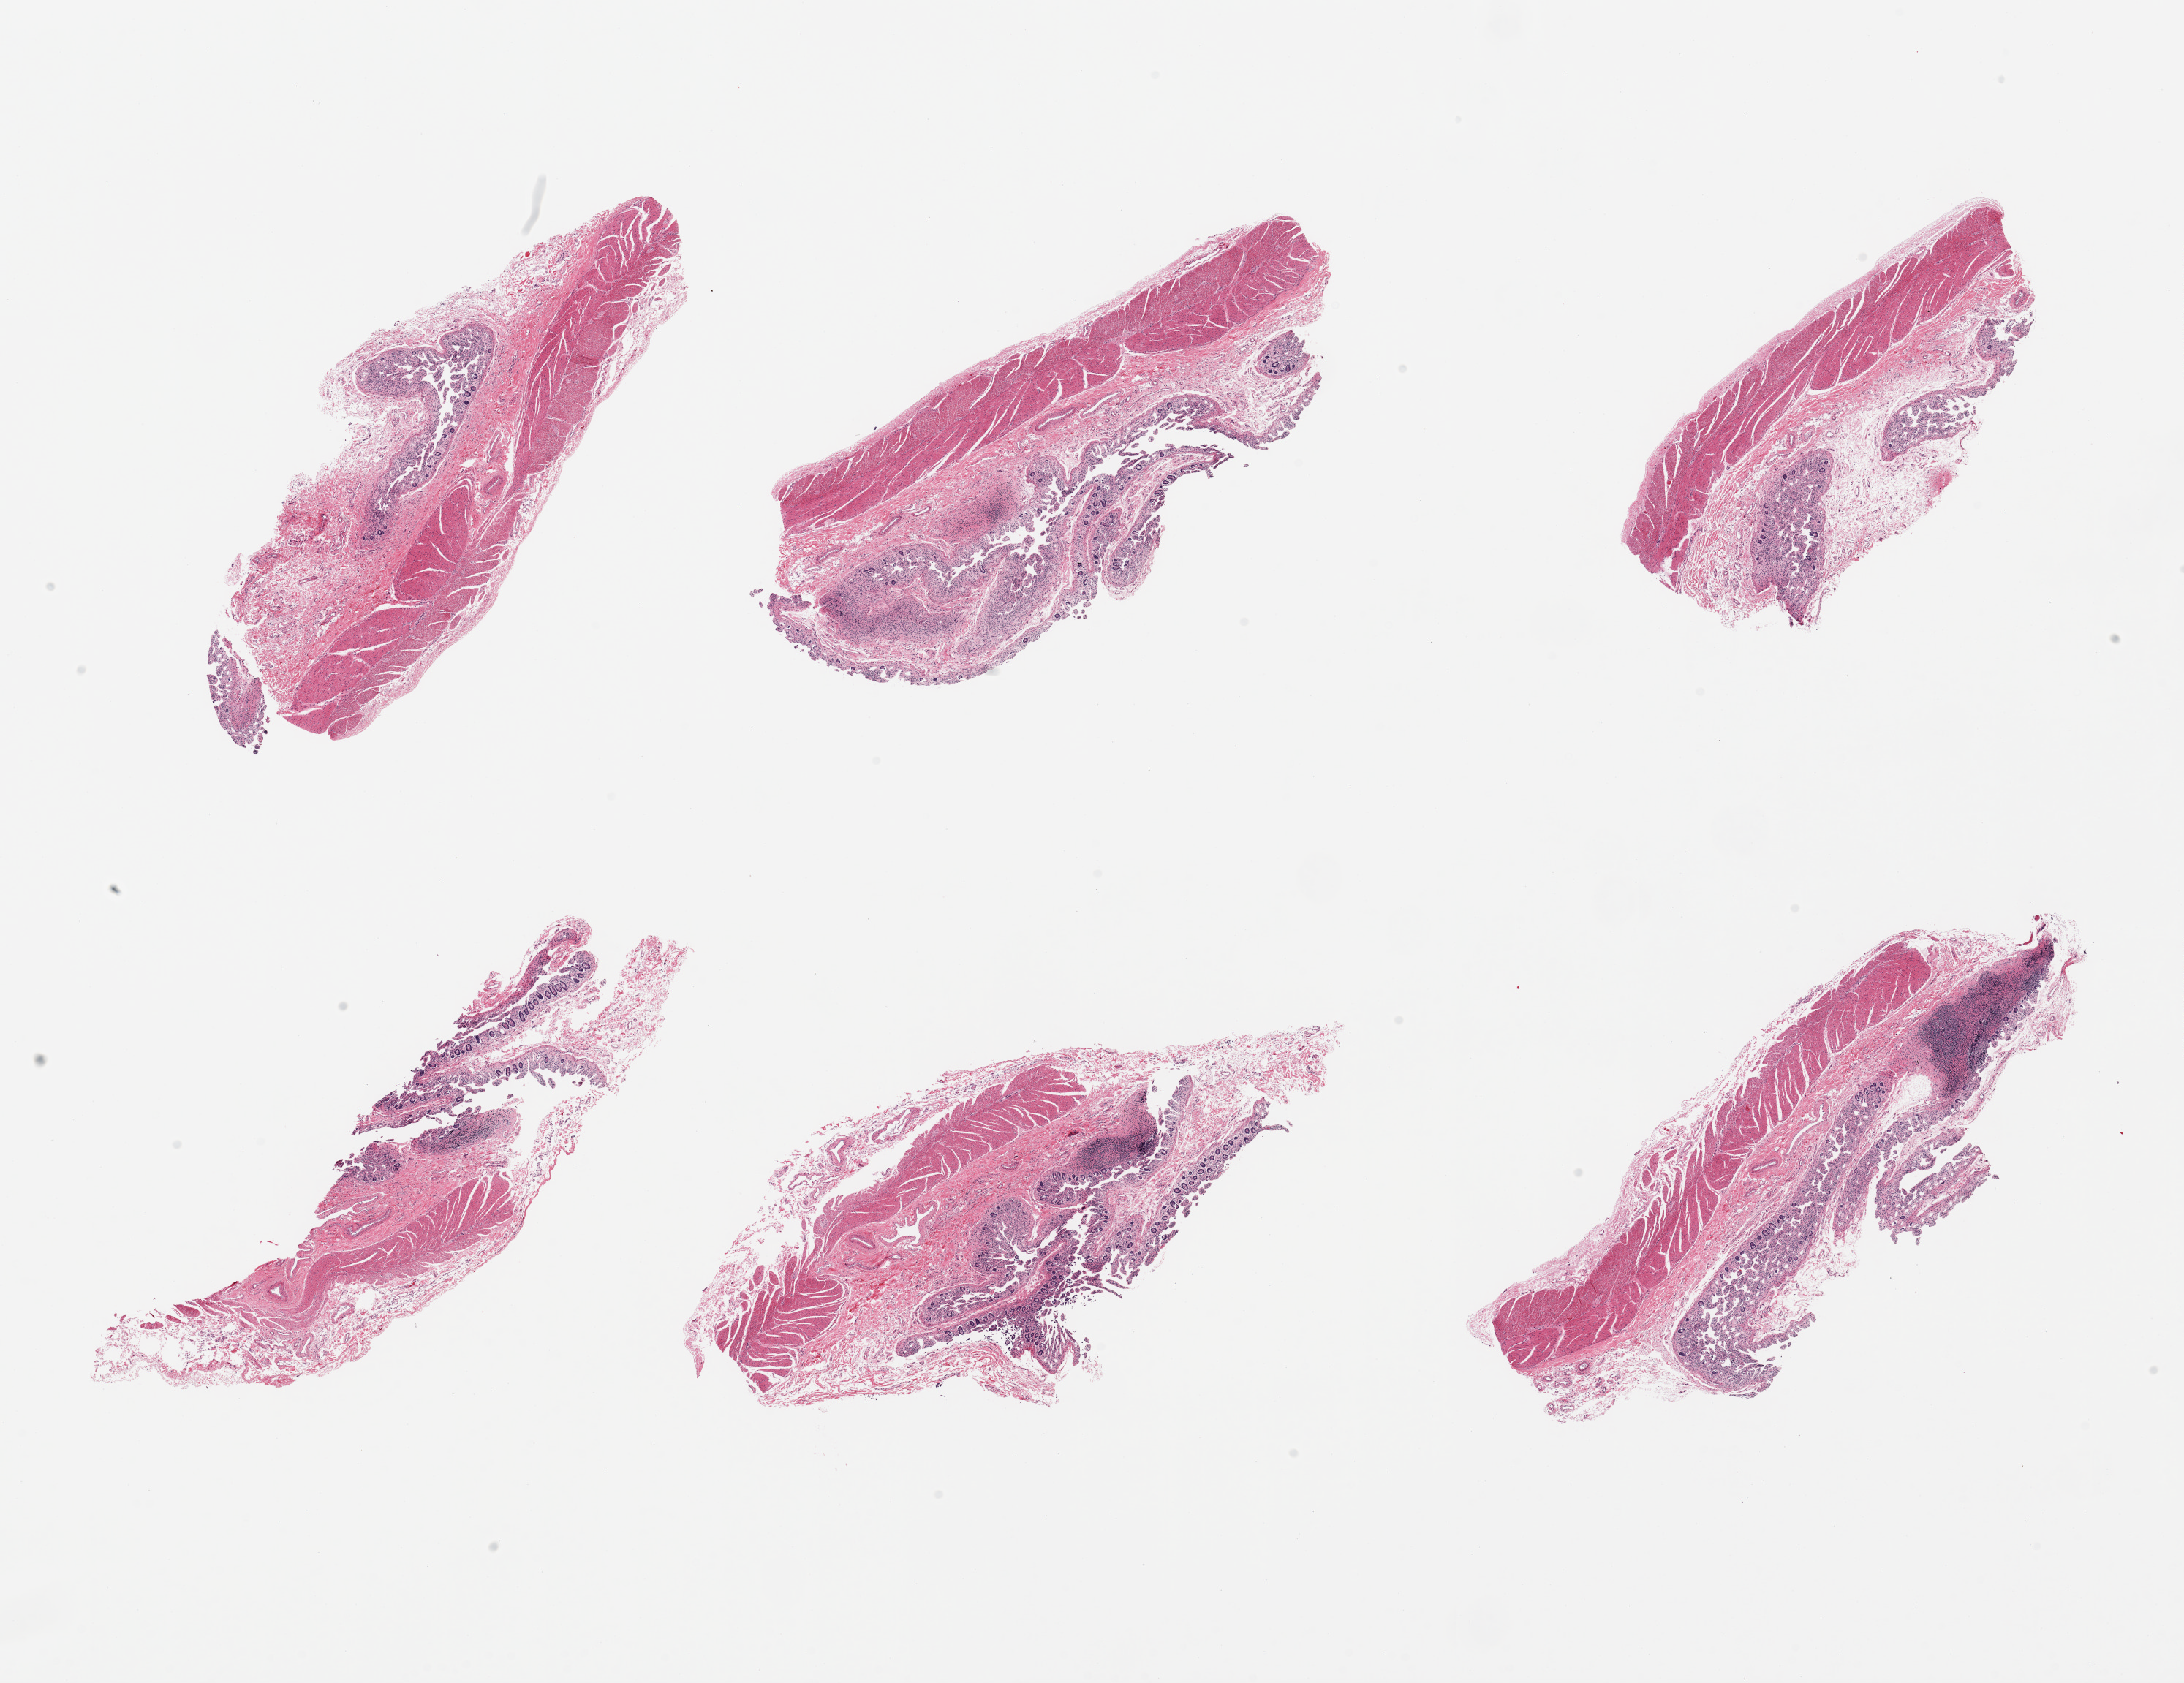
Digitized H&E-stained section, brightfield, shown as a low-resolution overview of the whole scanned area (about 23.6 x 18.2 mm). Male donor.
Specimen: PAXgene-fixed paraffin-embedded (PFPE) section; sampled site (target tissue): ileum; tissue donor sample.